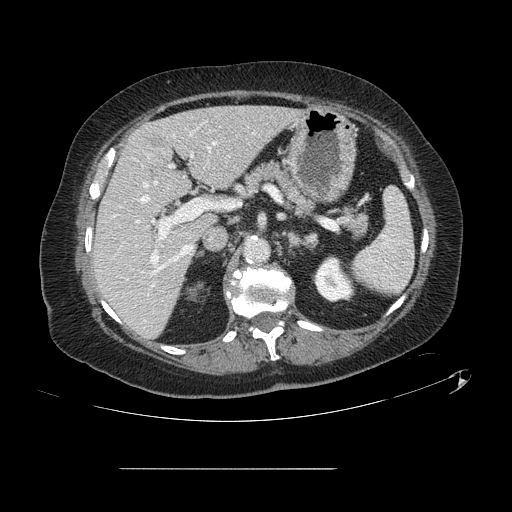
Contrast-enhanced abdominal CT, one axial slice; slice 73 of 148 in the series (ordered by position); 120 kVp; intravenous contrast given; soft-tissue window (W 400 / L 40 HU); 512 × 512 image matrix. Female patient, age 75 years. From the clinical record (not read from this slice): diagnosis: colorectal cancer liver metastases, imaged before liver resection; multiple liver metastases: no; largest metastasis: 2.4 cm; disease in both lobes: no.
Structures marked on this image (expert manual segmentation):
- hepatic veins: bounding box <141,142,216,255> (left, top, right, bottom; pixels)
- liver: <94,106,296,337>
- planned liver remnant (the part of the liver to remain after resection): <94,106,294,337>
- portal vein (with intrahepatic branches): <135,155,205,270>
- liver metastasis: <150,138,162,148>